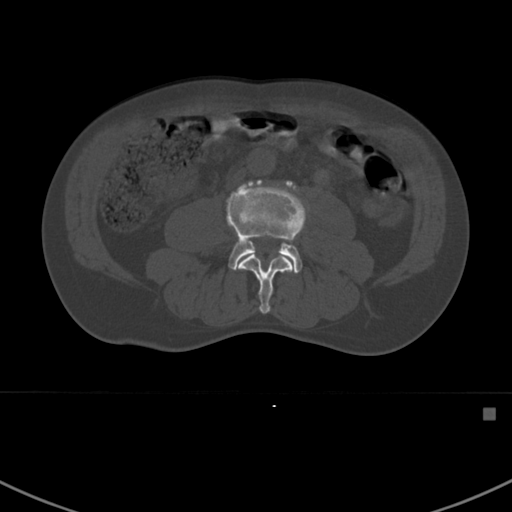
CT including the spine, one axial slice; position 252 of 412 along the scan axis; reconstruction kernel Br40s; bone window (W 1800 / L 400 HU); 512 × 512 image matrix, field of view 358 × 358 mm. Male patient, age 59 years. Case-level facts recorded for this patient, not image findings: primary cancer: prostate.
Annotated regions visible in this slice (semi-automatically segmented with operator editing):
- L3 vertebra: bounding box [x1, y1, x2, y2] px = [236, 252, 295, 314]
- L4 vertebra: [226, 178, 307, 273]